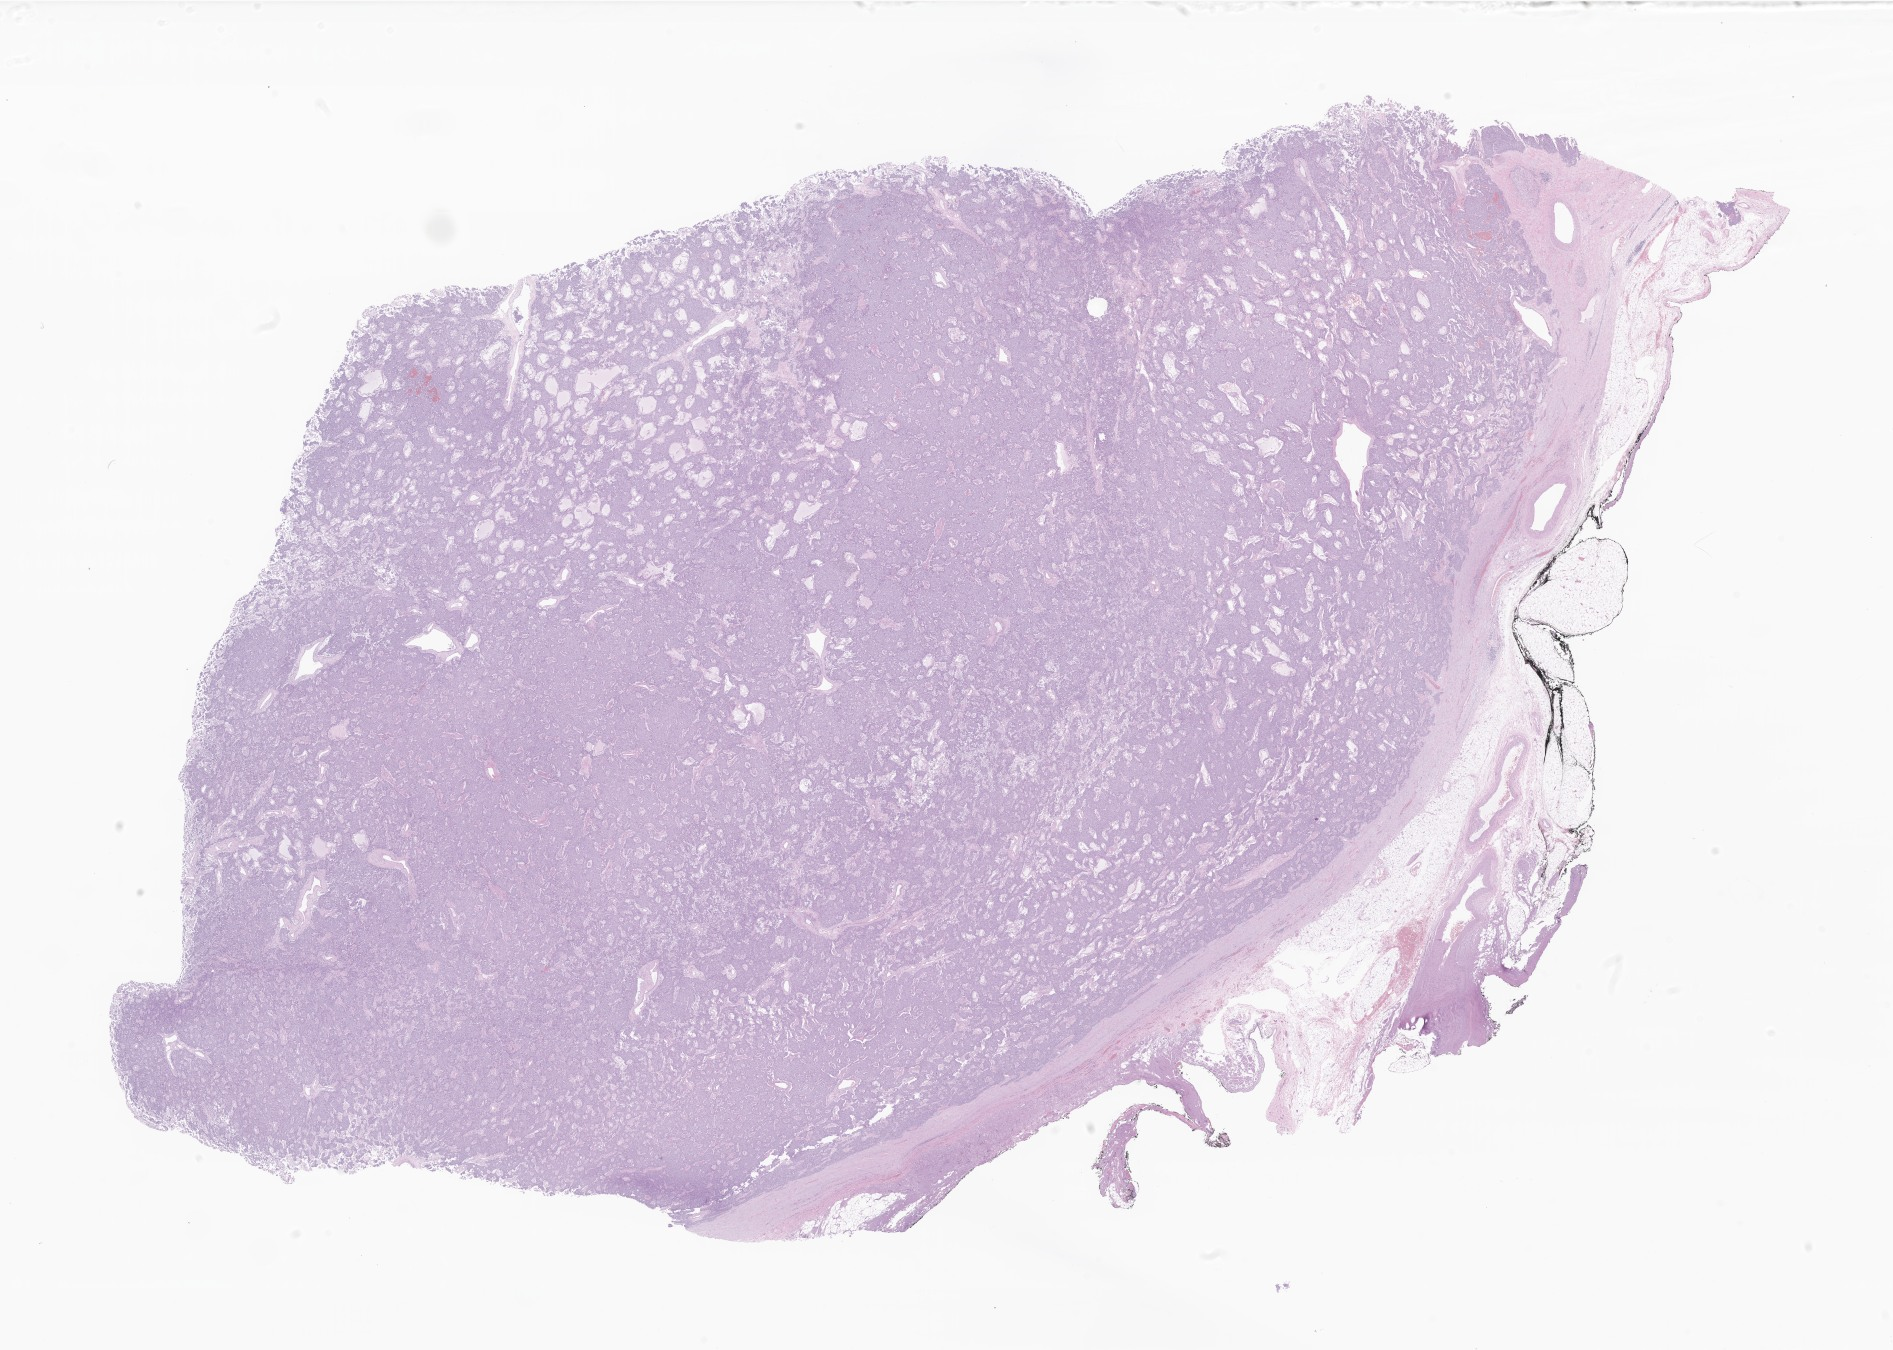
Digitized hematoxylin and eosin (H&E)-stained section of tumor tissue from the pancreas — shown as a low-resolution overview of the whole scanned area (about 31.9 x 22.8 mm). Formalin-fixed paraffin-embedded section. Patient: female, age 187 months.
Diagnosis: Vipoma.